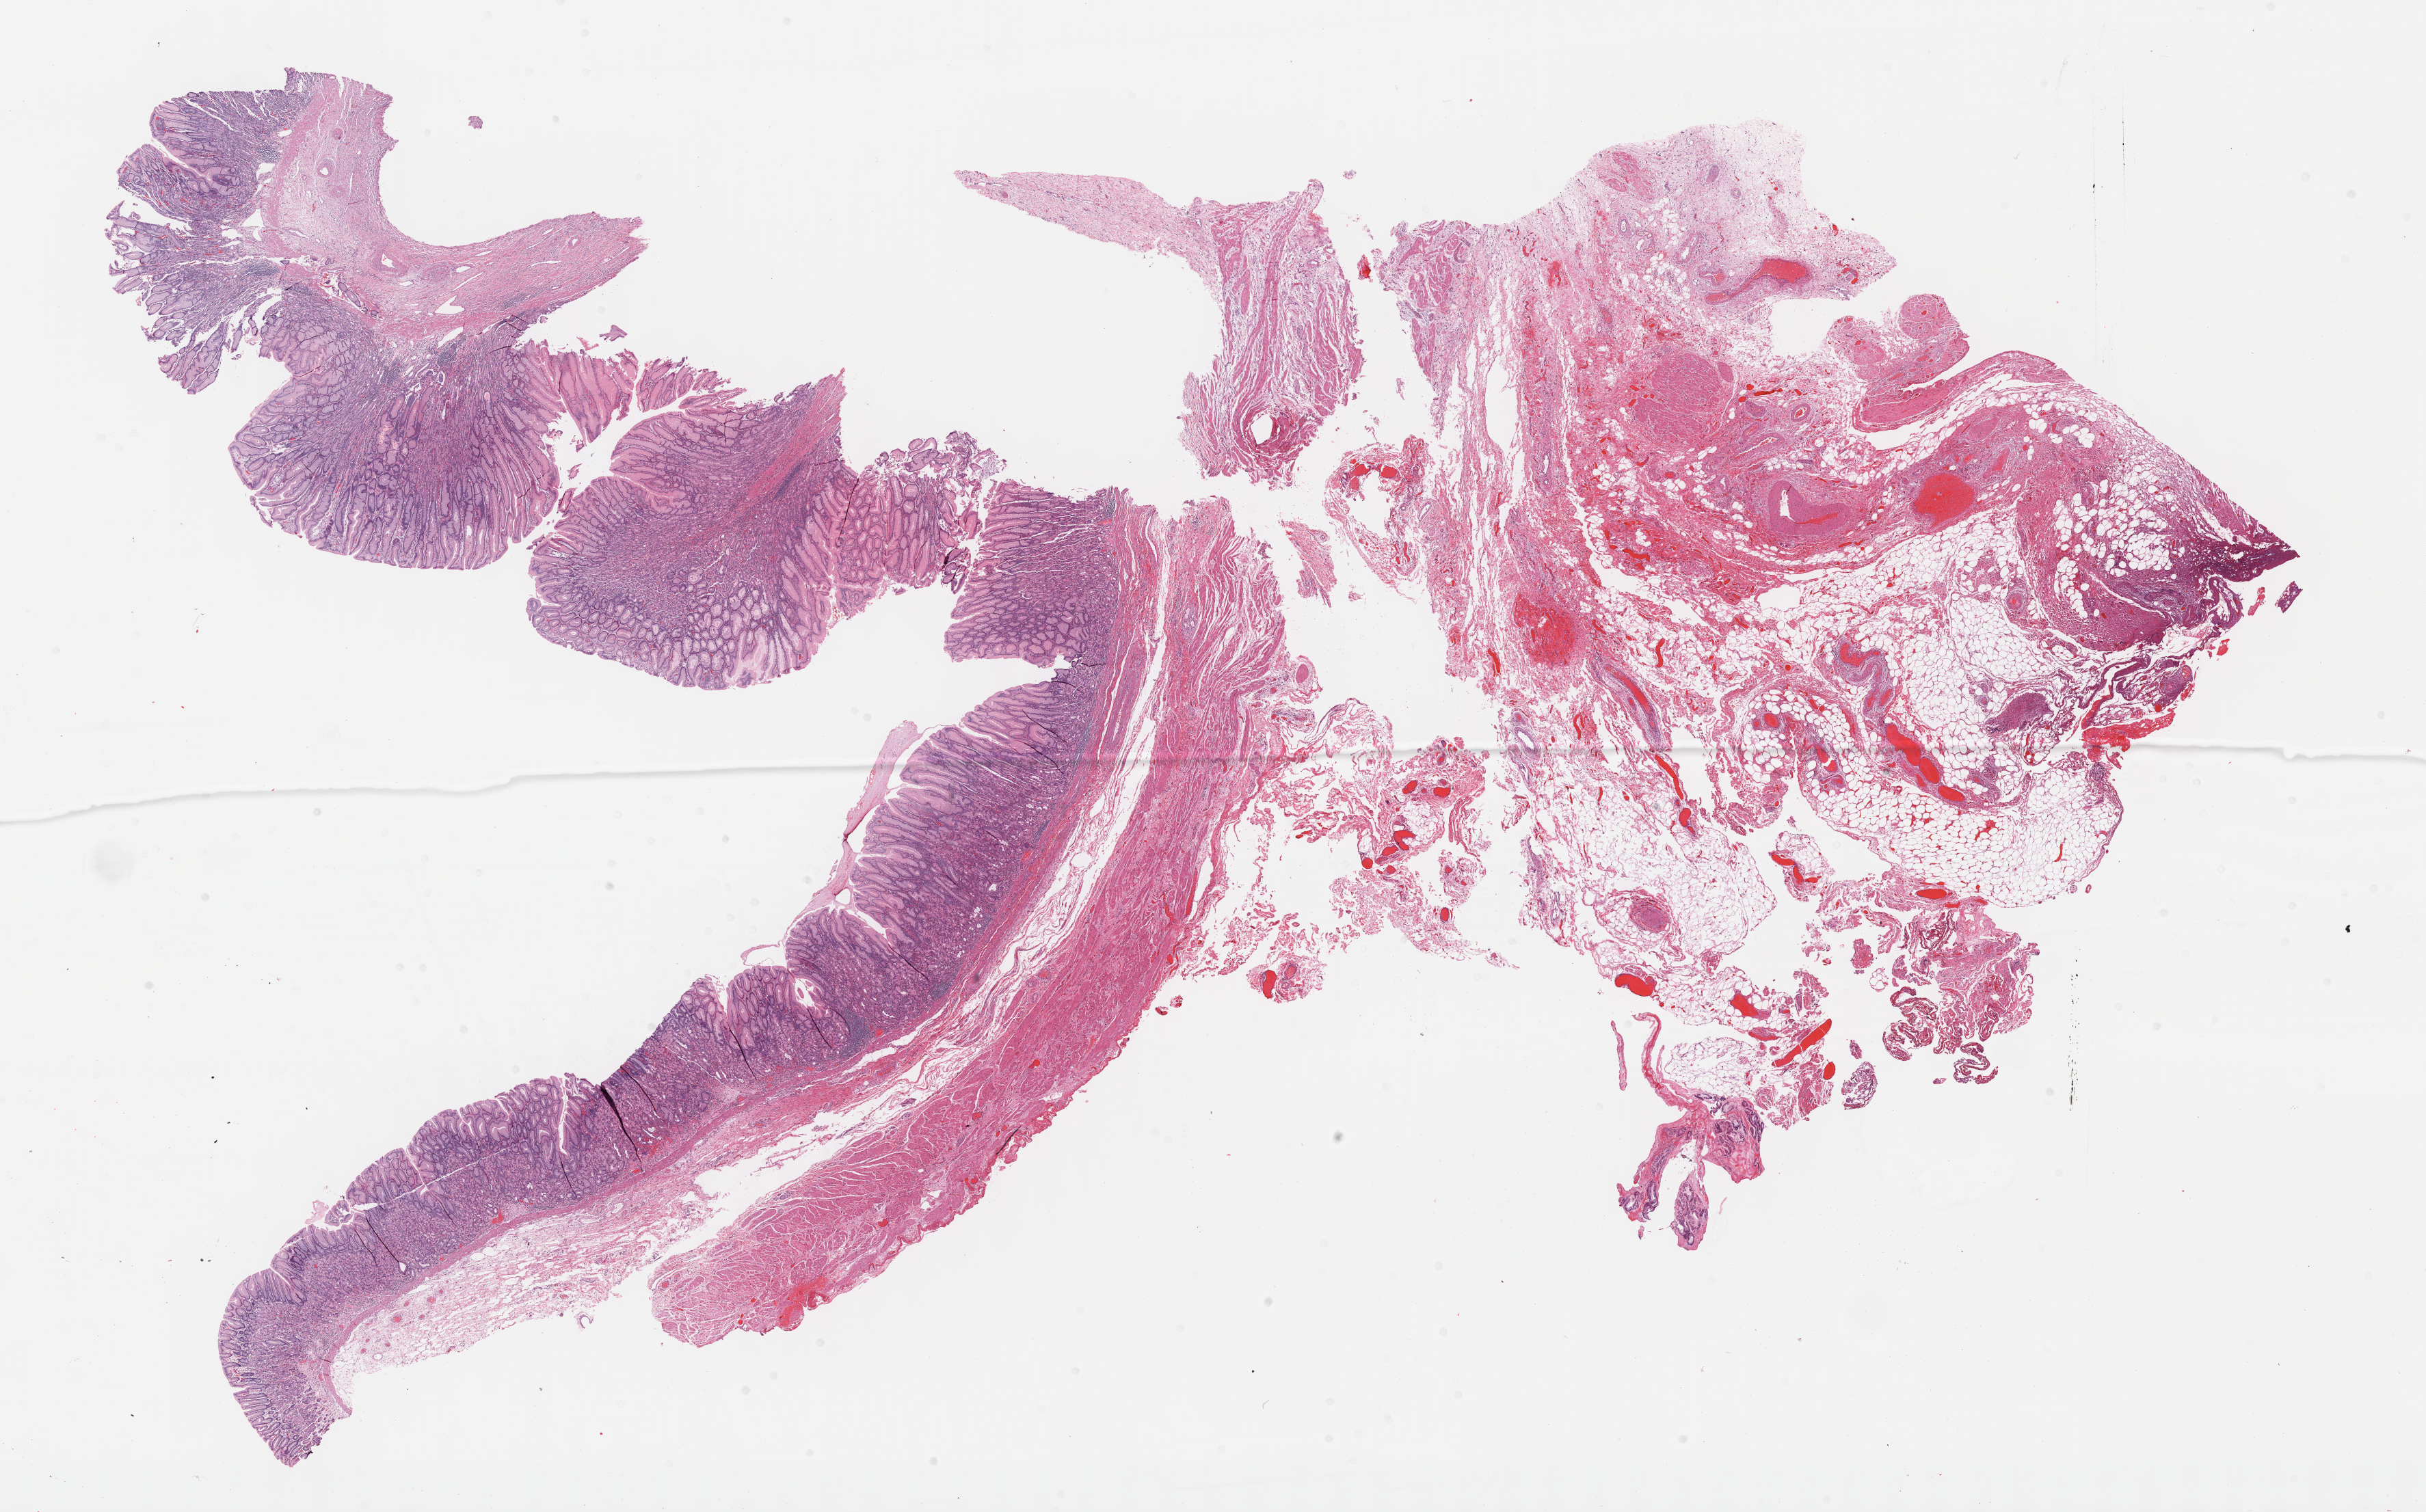
Whole-slide histology image, H&E, shown as a low-resolution overview of the whole scanned area (about 28.7 x 17.9 mm, acquisition: 40x scan). Formalin-fixed paraffin-embedded (FFPE) diagnostic section. Primary tumour sample from the stomach. Female patient; age at initial diagnosis 58 years.
Histologic diagnosis: Leiomyosarcoma, NOS.